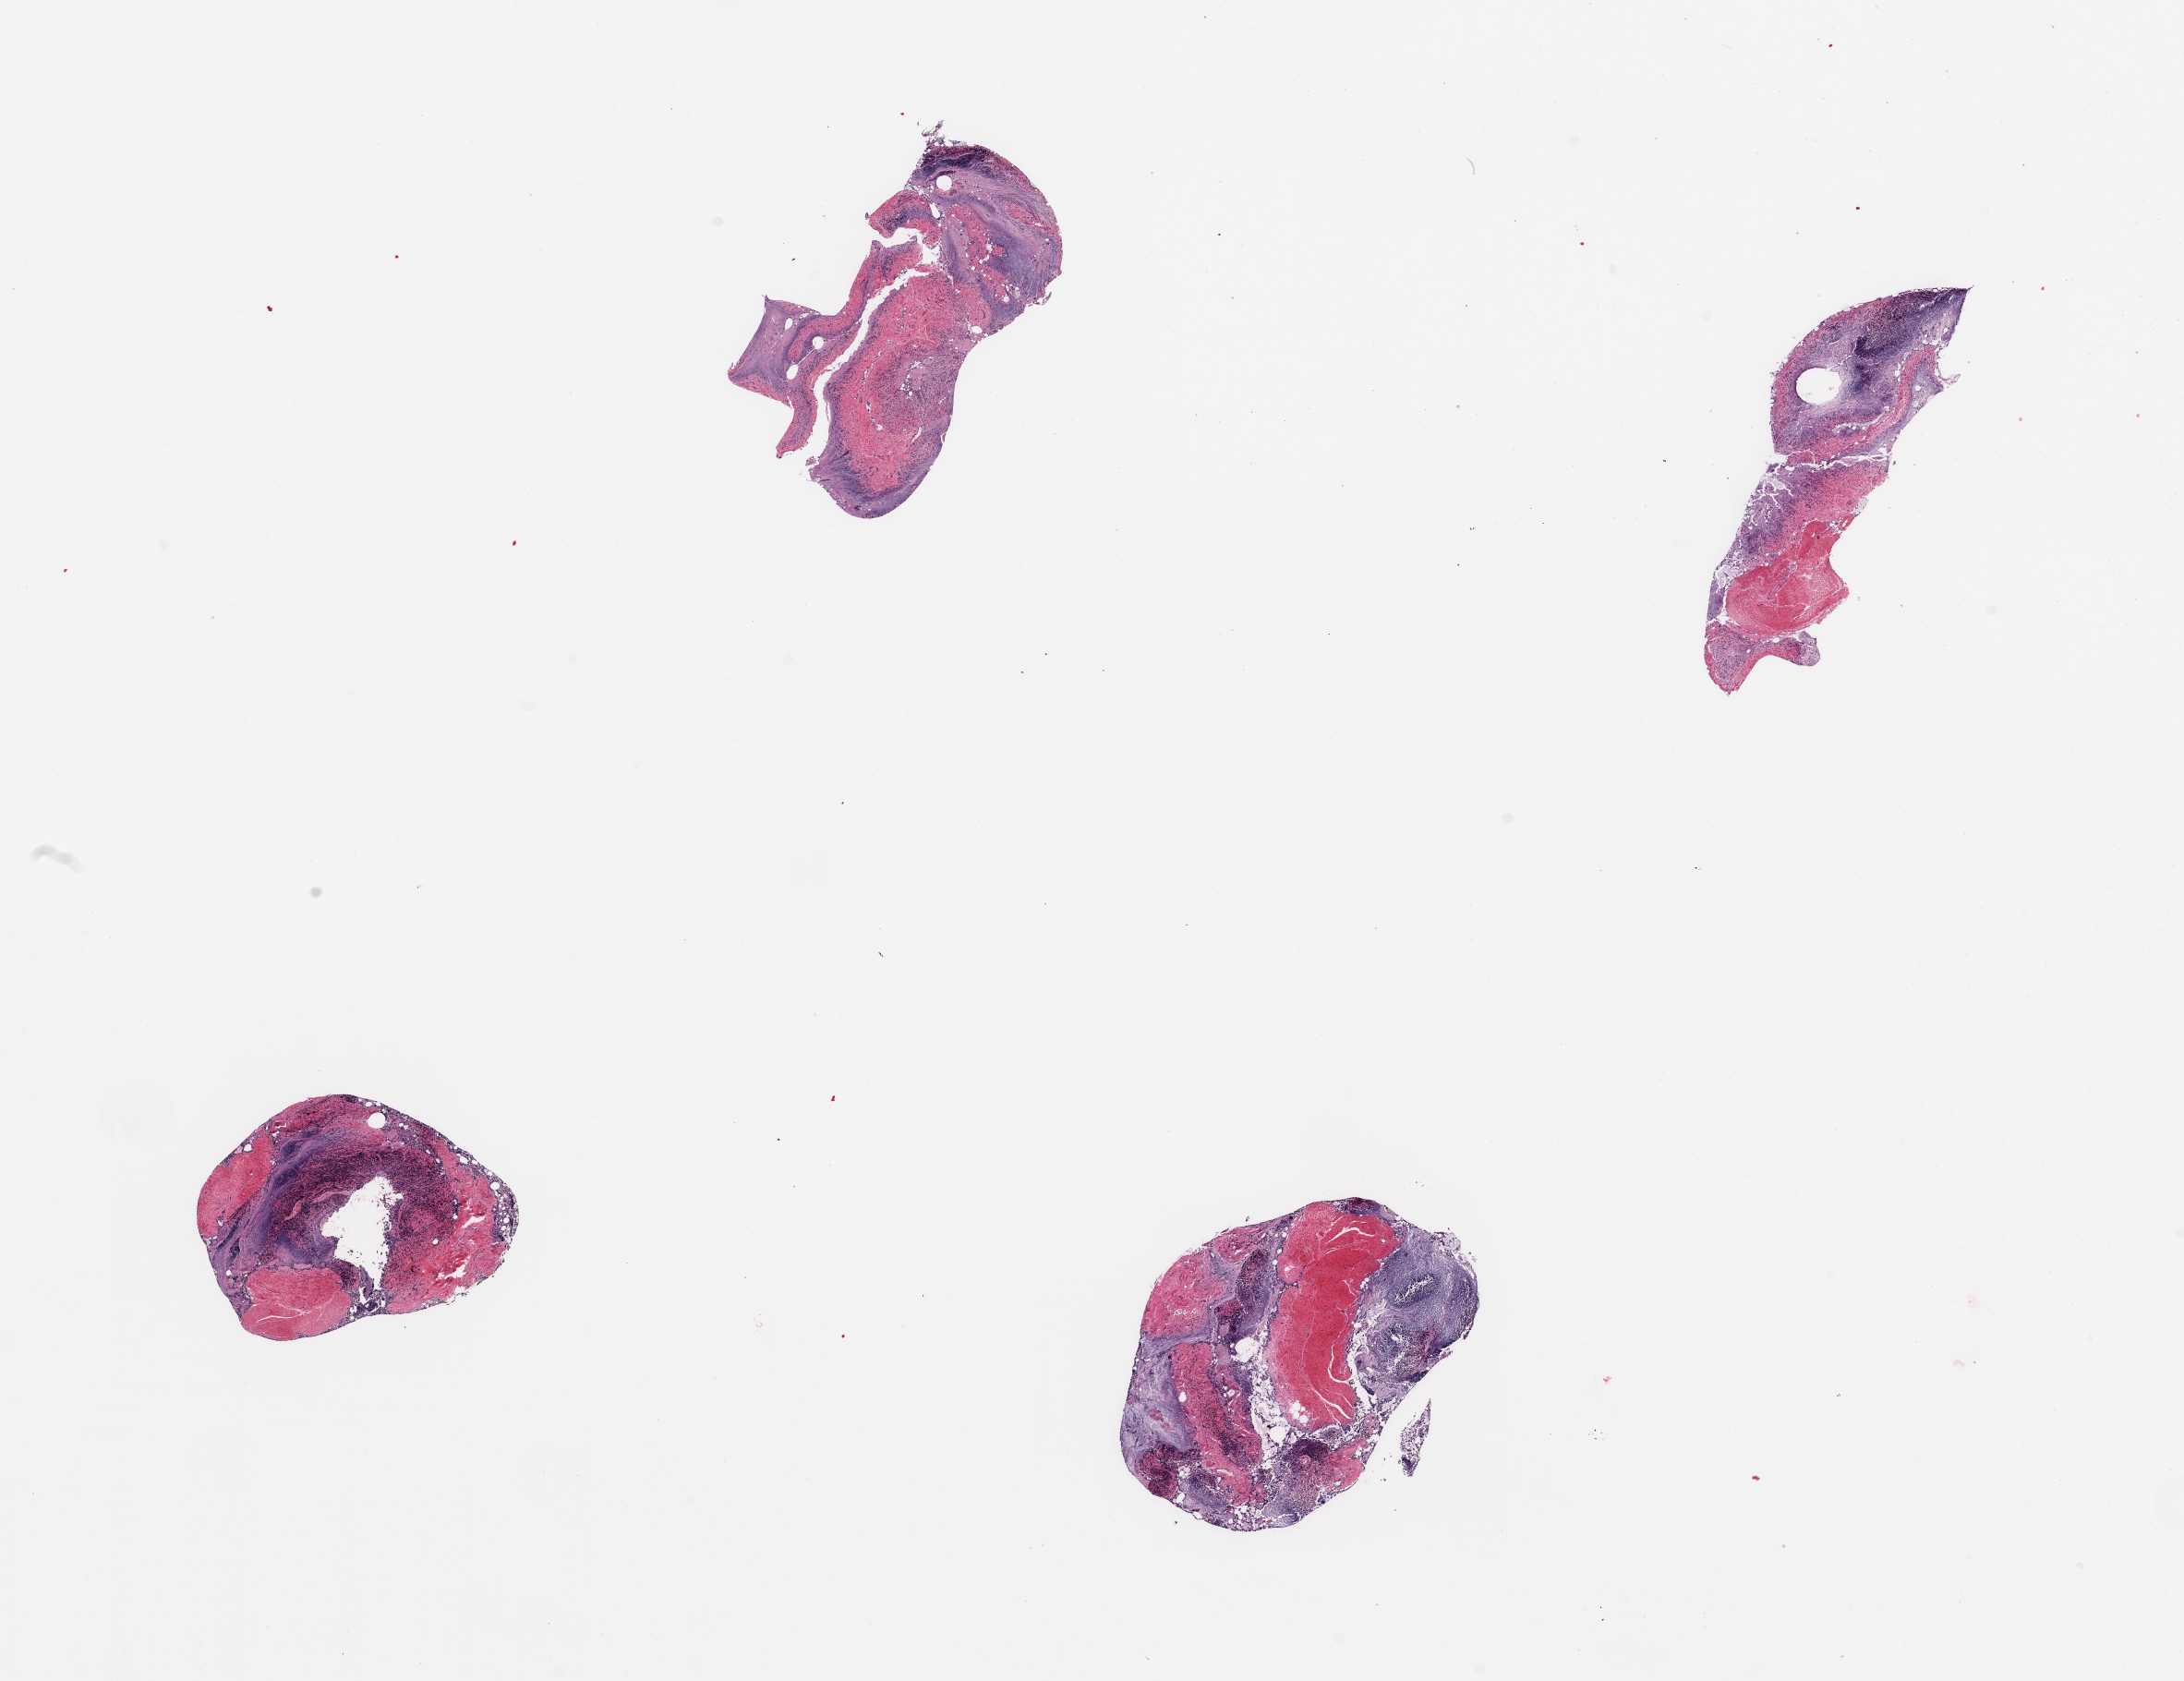
Whole-slide image, haematoxylin and eosin stain, brightfield — shown as a low-resolution overview of the whole scanned area (about 18.7 x 14.4 mm), PAXgene-fixed paraffin-embedded (PFPE) section, target tissue: ileum, tissue donor sample.
* reviewer comment on this tissue sample: 4 pieces; predominantly autolyzed mucosa, residual lymphoid component too limited for analysis, muscularis (not target) also present